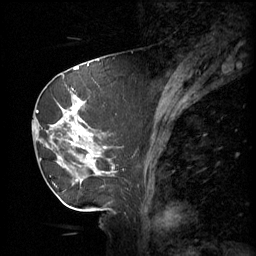
Breast MRI (dynamic contrast-enhanced), one sagittal slice; position 22 of 60 along the scan axis; 3 images stored at this slice position (order not interpretable as contrast timing); 1.5 T; TE 4.2 ms, TR 11 ms; 2 mm slice thickness; 256 × 256 image matrix, field of view 220 × 220 mm. Female patient, age 69 years.
Outlined on this slice (semi-automatically segmented with operator editing):
- analysis volume of interest (the breast-tissue region the enhancement analysis was run in; not a lesion): bounding box (x1, y1, x2, y2) in pixels: (36, 88, 116, 189)
- tumour enhancement mask (voxels above the 70 % enhancement threshold inside the analysis volume of interest): (37, 96, 96, 183)